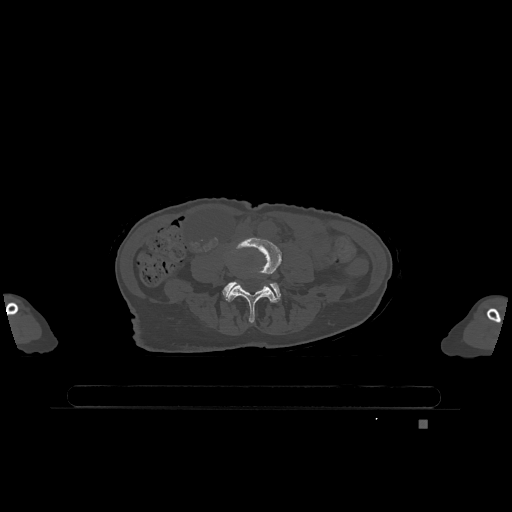
CT including the spine, one axial slice; bone window (W 1800 / L 400 HU); 0.5 mm slice thickness; 512 × 512 image matrix. Patient: female, 74 years. Case-level facts recorded for this patient, not image findings: primary cancer: lung.
Structures marked on this image (semi-automatically segmented with operator editing):
- L4 vertebra: bounding box (x1, y1, x2, y2) in pixels: (226, 237, 282, 323)
- L5 vertebra: (222, 281, 281, 302)